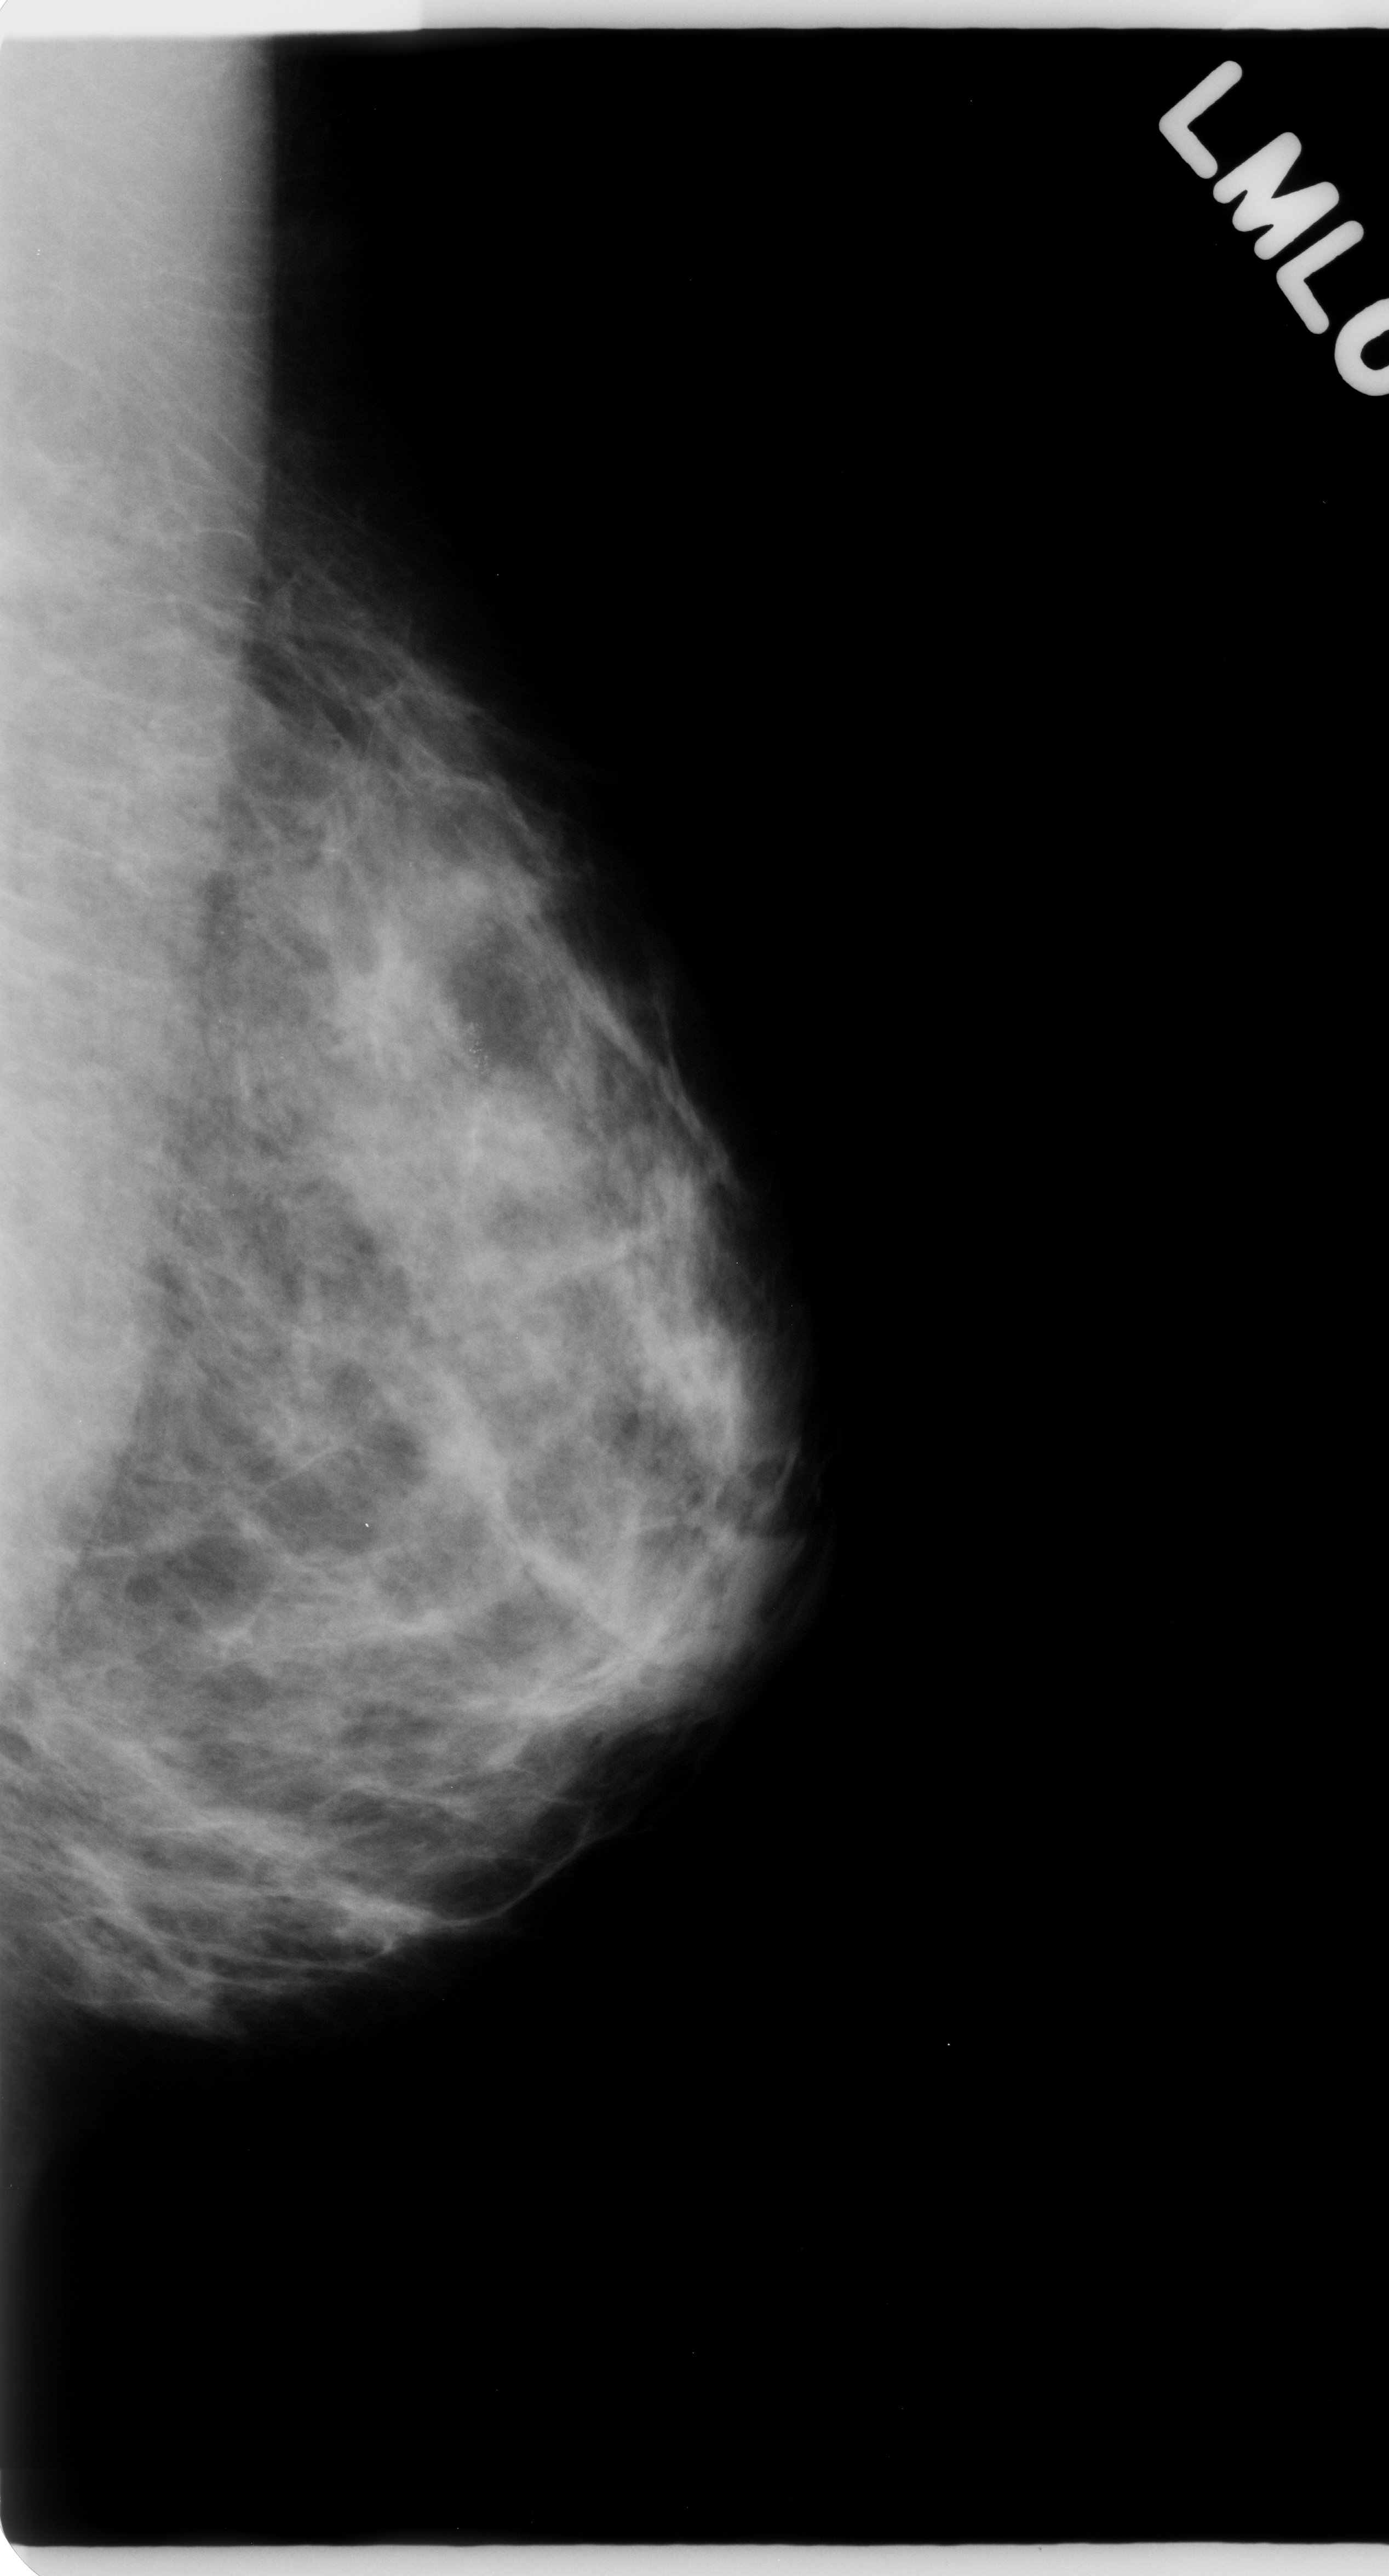
Digitized screen-film mammogram; left breast; MLO view.
Abnormality record for this image: calcifications, morphology pleomorphic, distribution clustered; BI-RADS assessment category 5; subtlety rating 4 on a 1 (subtle) to 5 (obvious) scale; pathology result (as recorded, not read from the image): malignant.